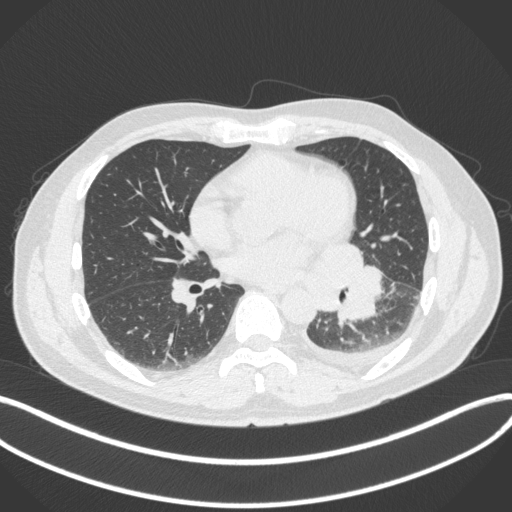
Chest CT, one axial slice; position 165 of 350 along the scan axis; 120 kVp; lung window (W 1500 / L -600 HU); 1 mm slice thickness; 512 × 512 image matrix, field of view 400 × 400 mm. Male patient, age 58 years. Case-level facts recorded for this patient, not image findings: clinical TNM (as recorded): T3 N1 M1b.
Outlined on this slice (bounding box drawn by a radiologist):
- lung tumour (recorded histology: small cell carcinoma): bounding box [x1, y1, x2, y2] px = [313, 238, 385, 332]